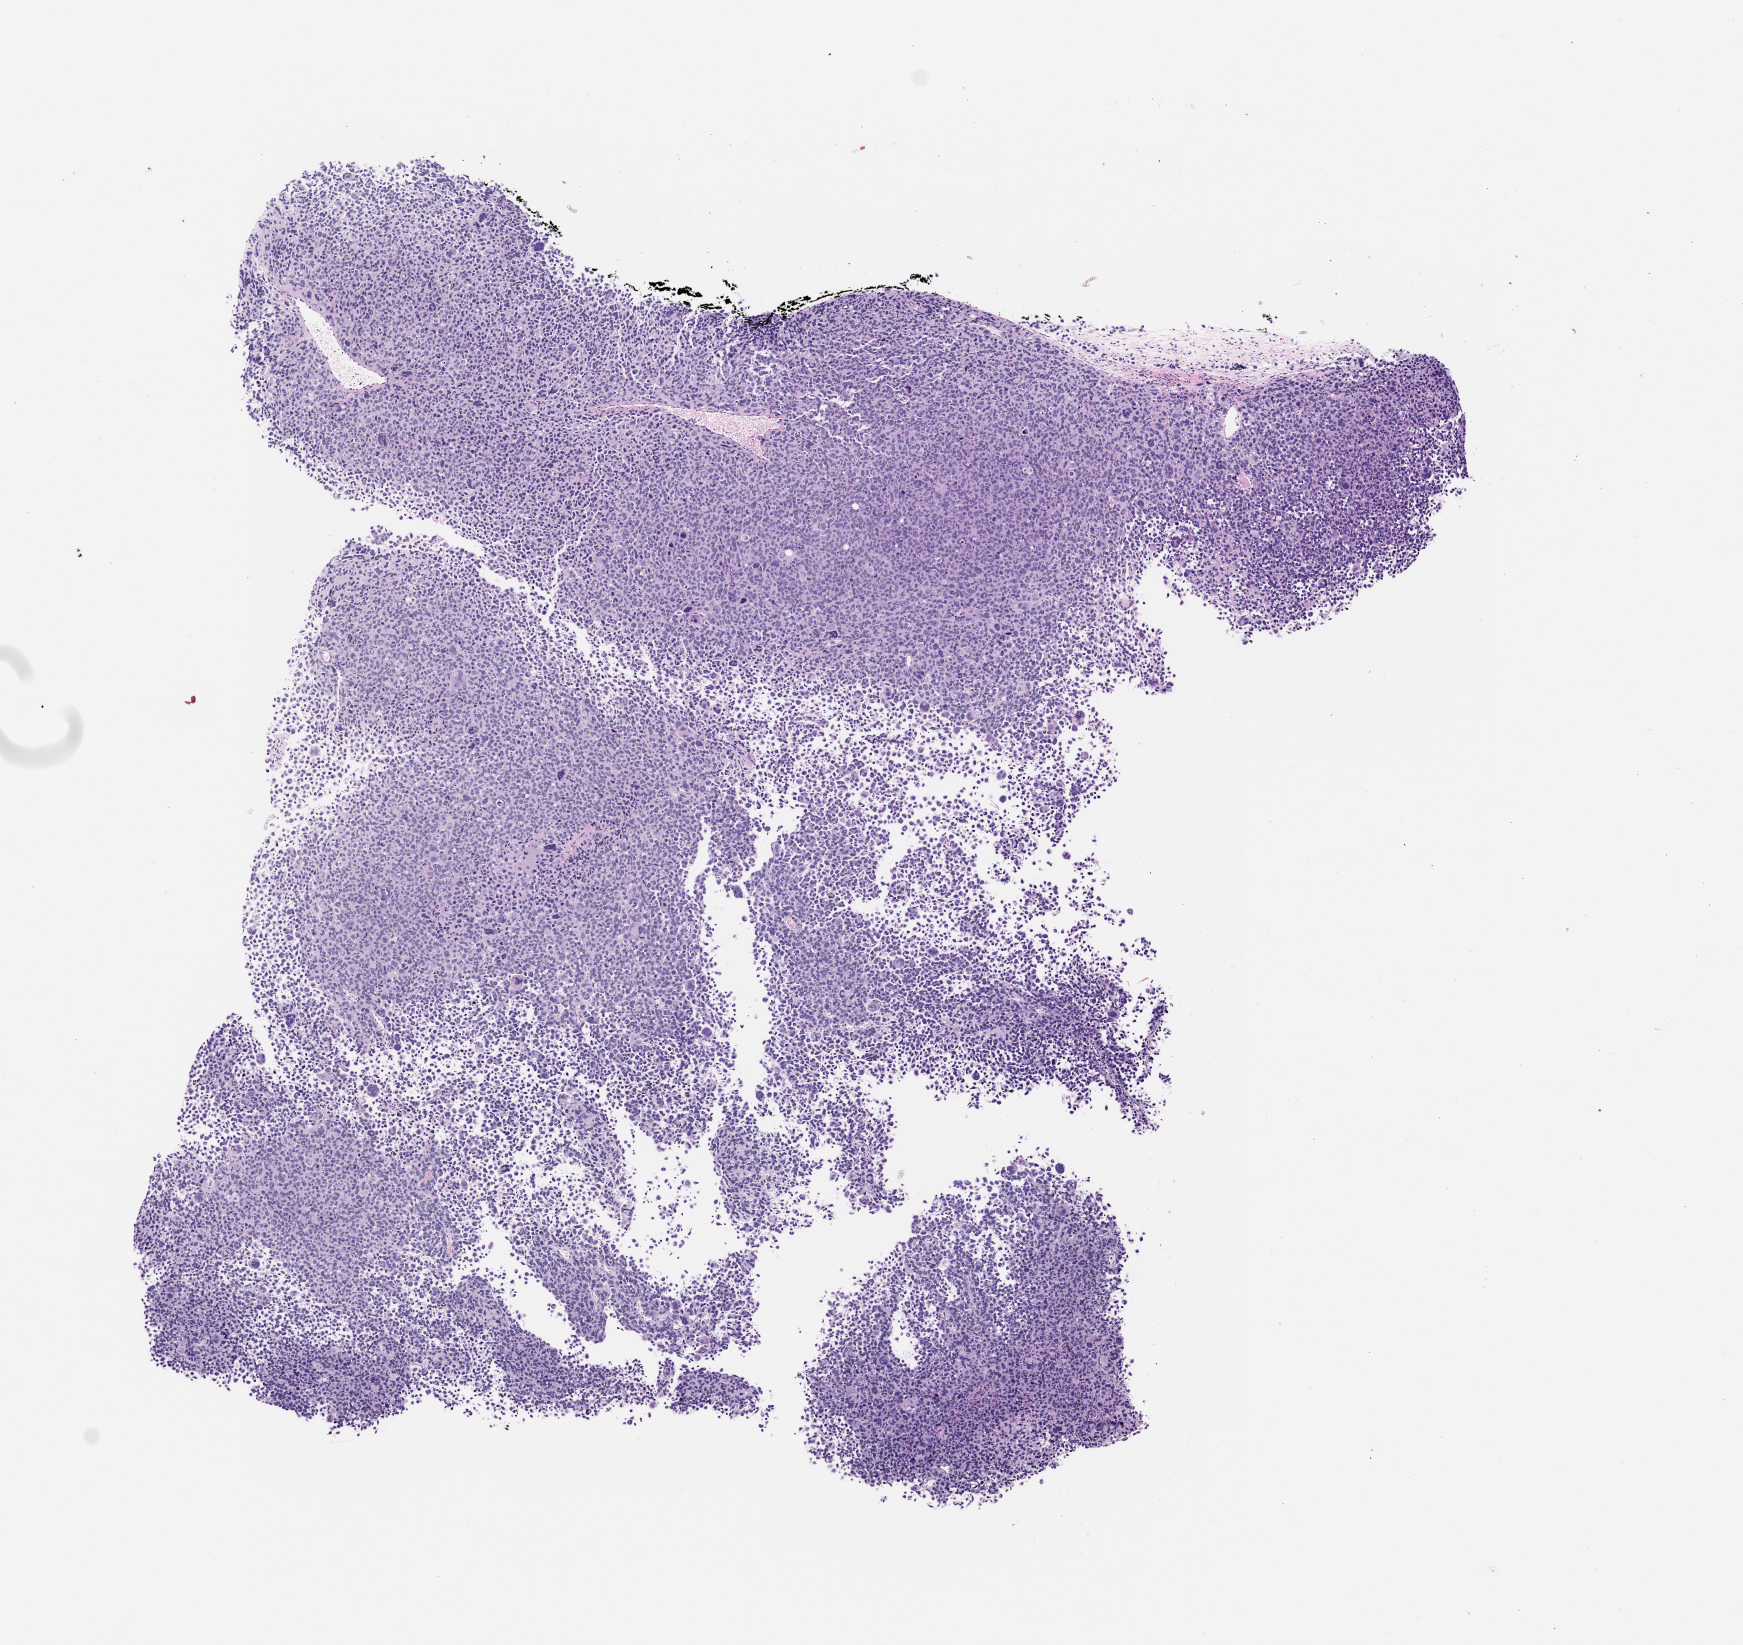
Haematoxylin and eosin whole-slide image of a patient-derived xenograft (PDX) tumor grown in a mouse, passage 0 — a low-resolution overview of the entire scanned area, about 7.0 x 6.6 mm; formalin-fixed paraffin-embedded section; tumor site category: skin.
* originating patient diagnosis: Melanoma